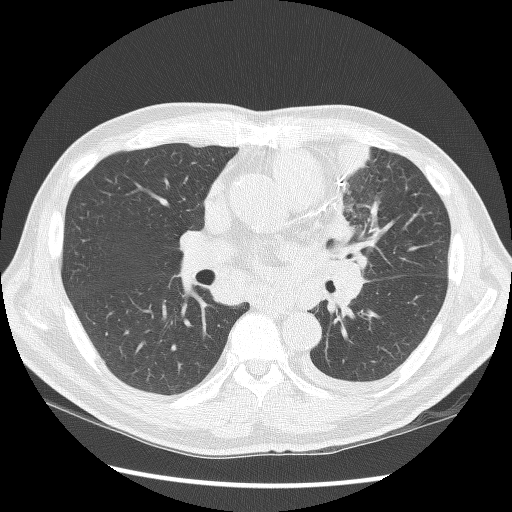
Chest CT (low-dose screening protocol), one axial image; second screening round (one year after baseline); lung window (W 1500 / L -600 HU); 2.5 mm slice thickness; lung (sharp) reconstruction kernel (BONE); 512 × 512 image matrix, field of view 360 × 360 mm. Male participant, aged 64 years at enrolment.
Expert-annotated lung lesion, bounding box <306,128,395,278> (left, top, right, bottom; pixels). No non-calcified nodule or mass ≥4 mm was recorded by the screening reader at this exam. Official screen result: positive, other.